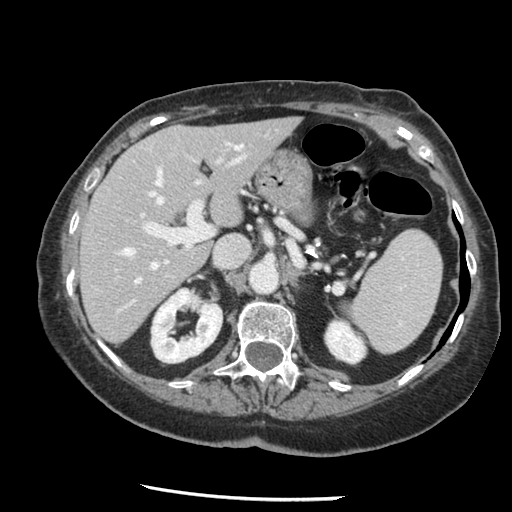
Contrast-enhanced abdominal CT, one axial slice. Slice 83 of 148 in the series (ordered by position). Reconstruction kernel STANDARD. 120 kVp. Soft-tissue window (W 400 / L 40 HU). 512 × 512 image matrix, field of view 330 × 330 mm. Female patient, age 85 years. From the clinical record (not read from this slice): diagnosis: colorectal cancer liver metastases, imaged before liver resection; multiple liver metastases: no; largest metastasis: 0.9 cm.
Annotated regions visible in this slice (expert manual segmentation):
- hepatic veins: bounding box <122,147,167,283> (left, top, right, bottom; pixels)
- liver: <81,118,299,342>
- planned liver remnant (the part of the liver to remain after resection): <81,118,299,342>
- portal vein (with intrahepatic branches): <141,139,231,247>